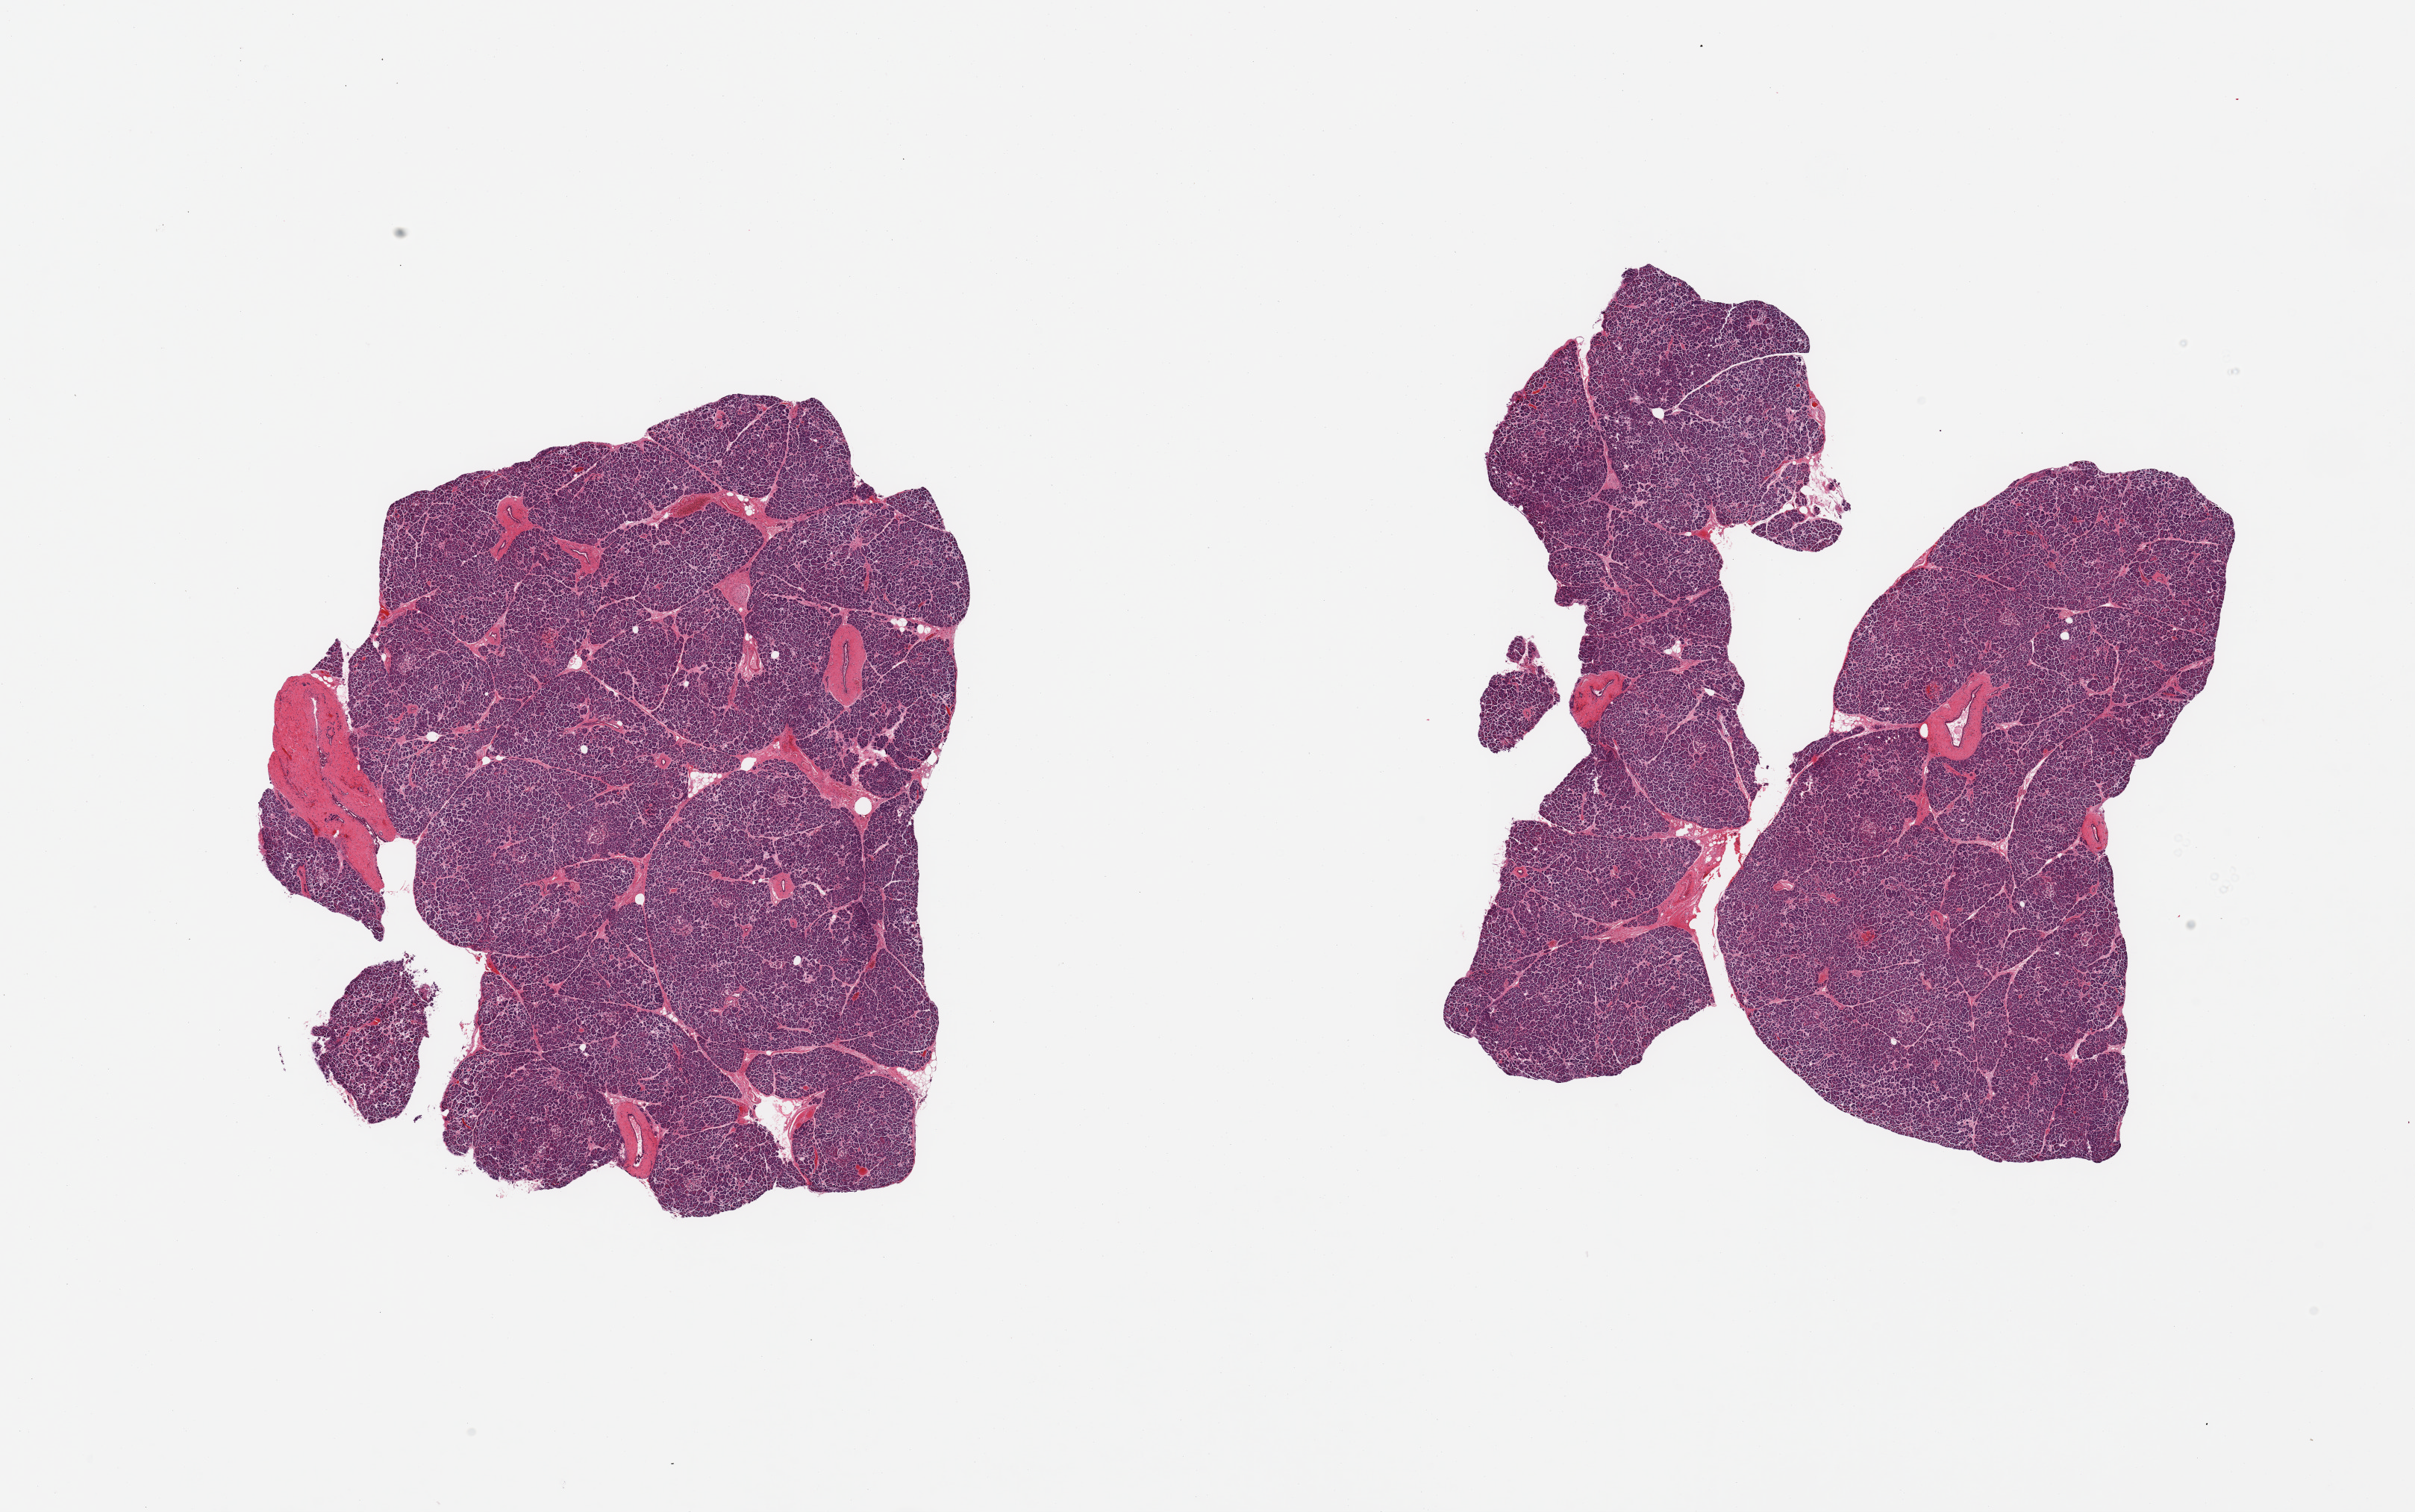
Digitized hematoxylin and eosin (H&E)-stained section, whole scanned area (about 25.6 x 16.0 mm) shown as a low-resolution overview; PAXgene-fixed paraffin-embedded (PFPE) section; sampled site (target tissue): pancreas; donor tissue sample. Male donor.
Pathologist's review note for this sample: 2 pieces; well trimmed; sparse islets.